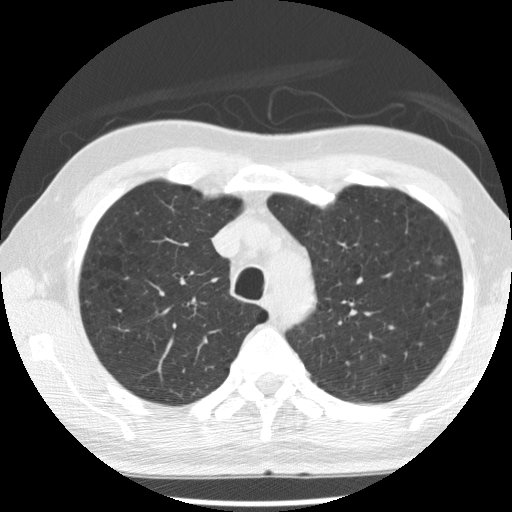
Chest CT (low-dose screening protocol), one axial image. Baseline annual screen. Lung window (W 1500 / L -600 HU). 2.5 mm slice thickness. Standard (soft-tissue) reconstruction kernel (STANDARD). Slice 62 of 277 in the series. 512 × 512 image matrix. Male, age 68 years at enrolment. Current smoker at enrolment.
Lesion marked by an expert reader, bounding box <424,248,461,282> (left, top, right, bottom; pixels). The exam's reader record, not a measurement of the box and not confirmed to be the same lesion: non-calcified nodule or mass ≥4 mm, left upper lobe, 5 × 5 mm, poorly defined margins, ground glass attenuation.